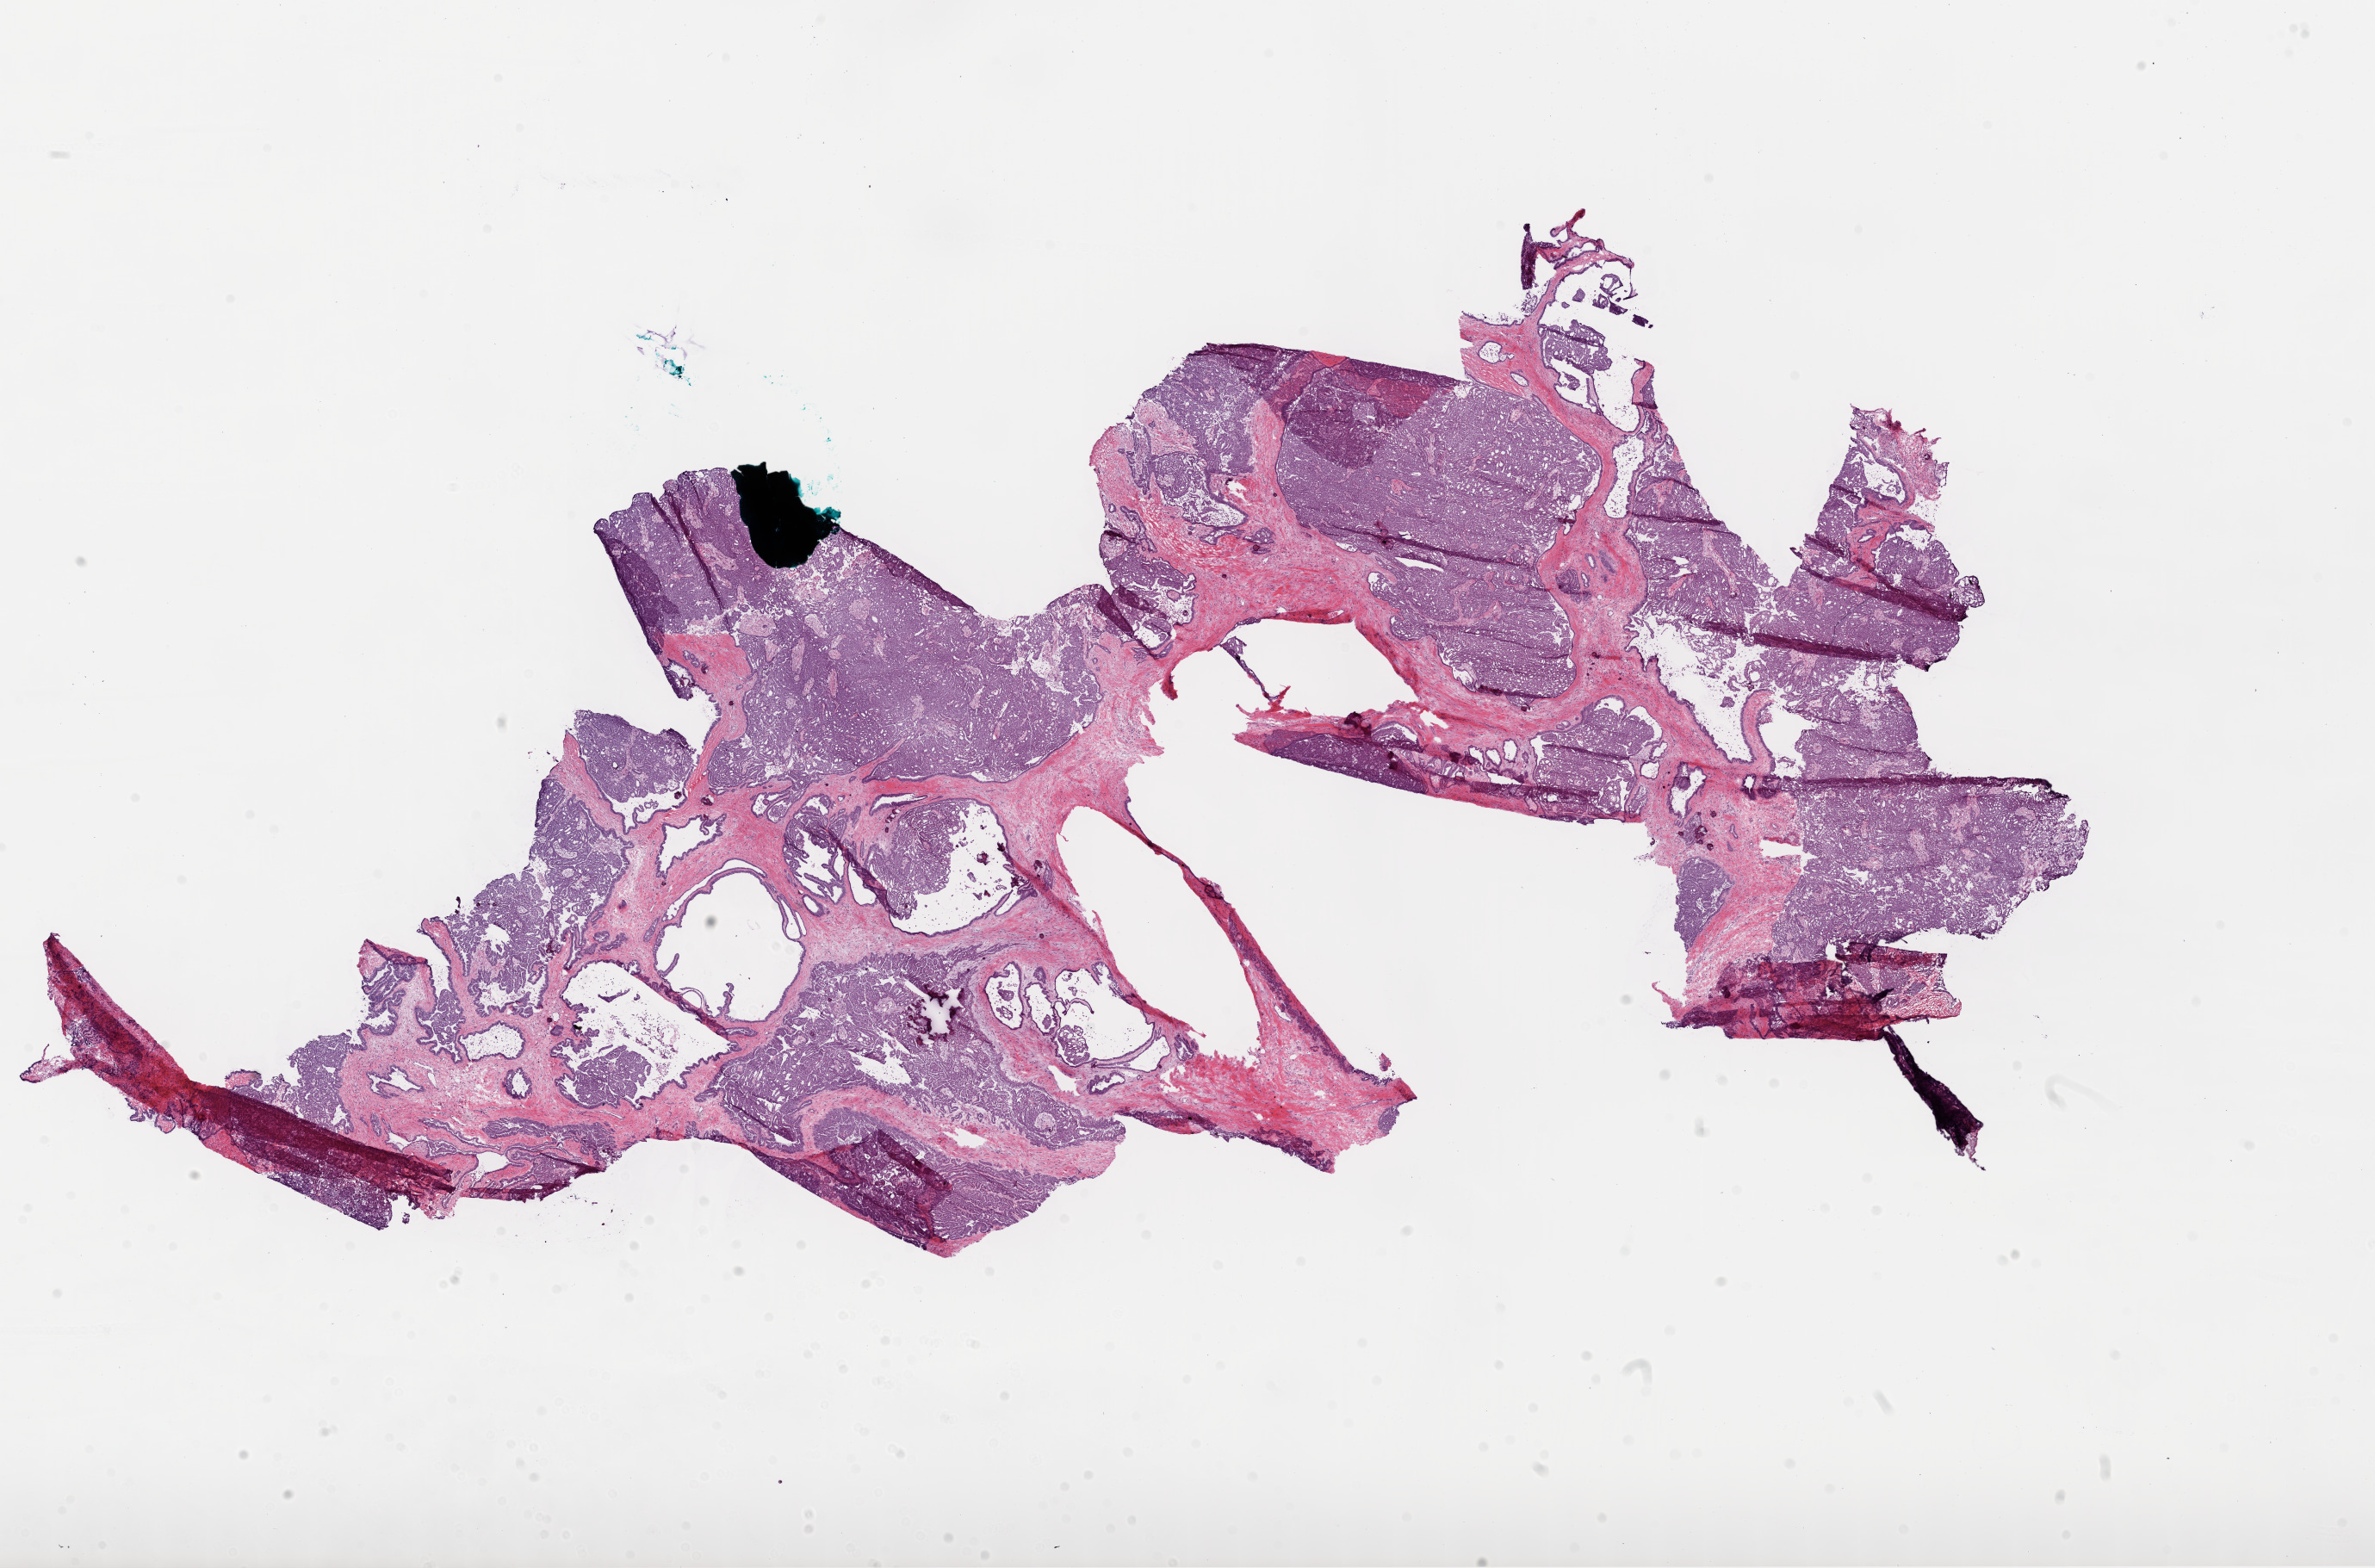
Digitized H&E tissue section (whole slide), shown as a low-resolution overview of the whole scanned area (about 22.2 x 14.7 mm); frozen section; ovary, primary tumour sample. Female, age 59 years at initial diagnosis. Slide review estimates, as recorded: tumour cells 64%, tumour nuclei 75%.
Diagnosis: Serous cystadenocarcinoma, NOS.